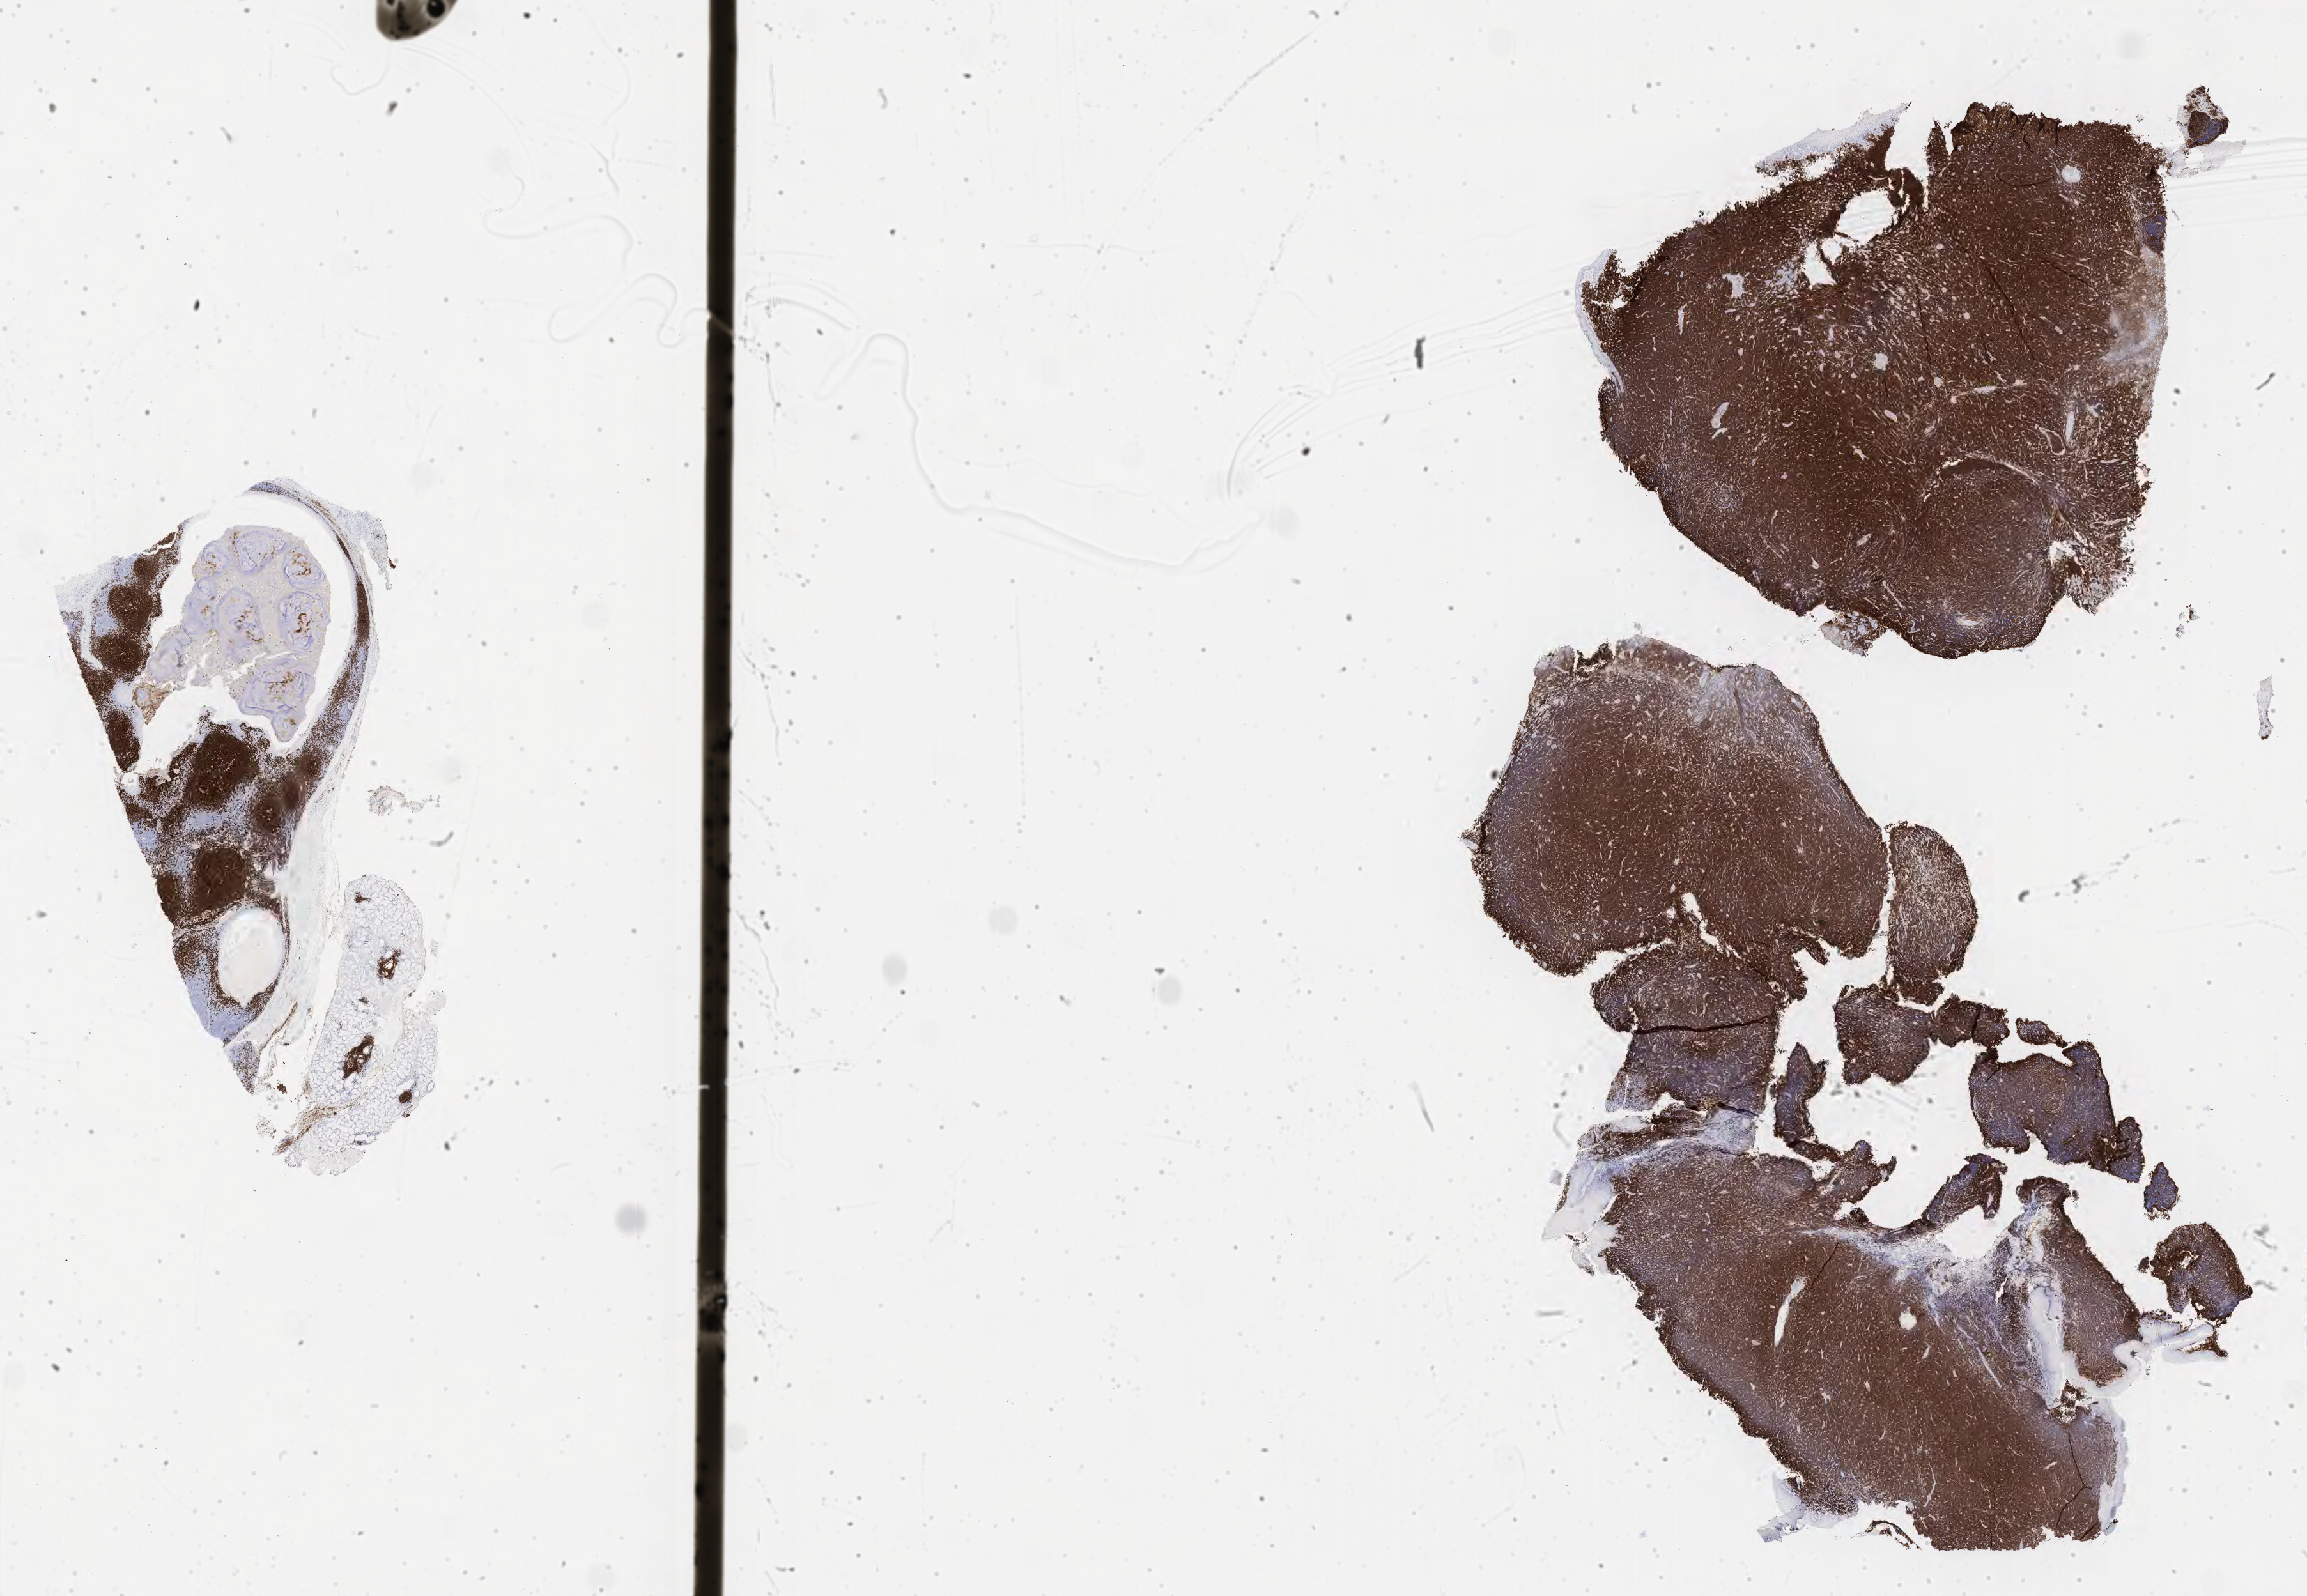
IHC for CD20, whole-slide image, whole scanned area (about 29.2 x 20.2 mm) shown as a low-resolution overview; tumor tissue. Patient: male, 22 years old.
Histologic diagnosis: Diffuse large B-cell lymphoma, NOS.